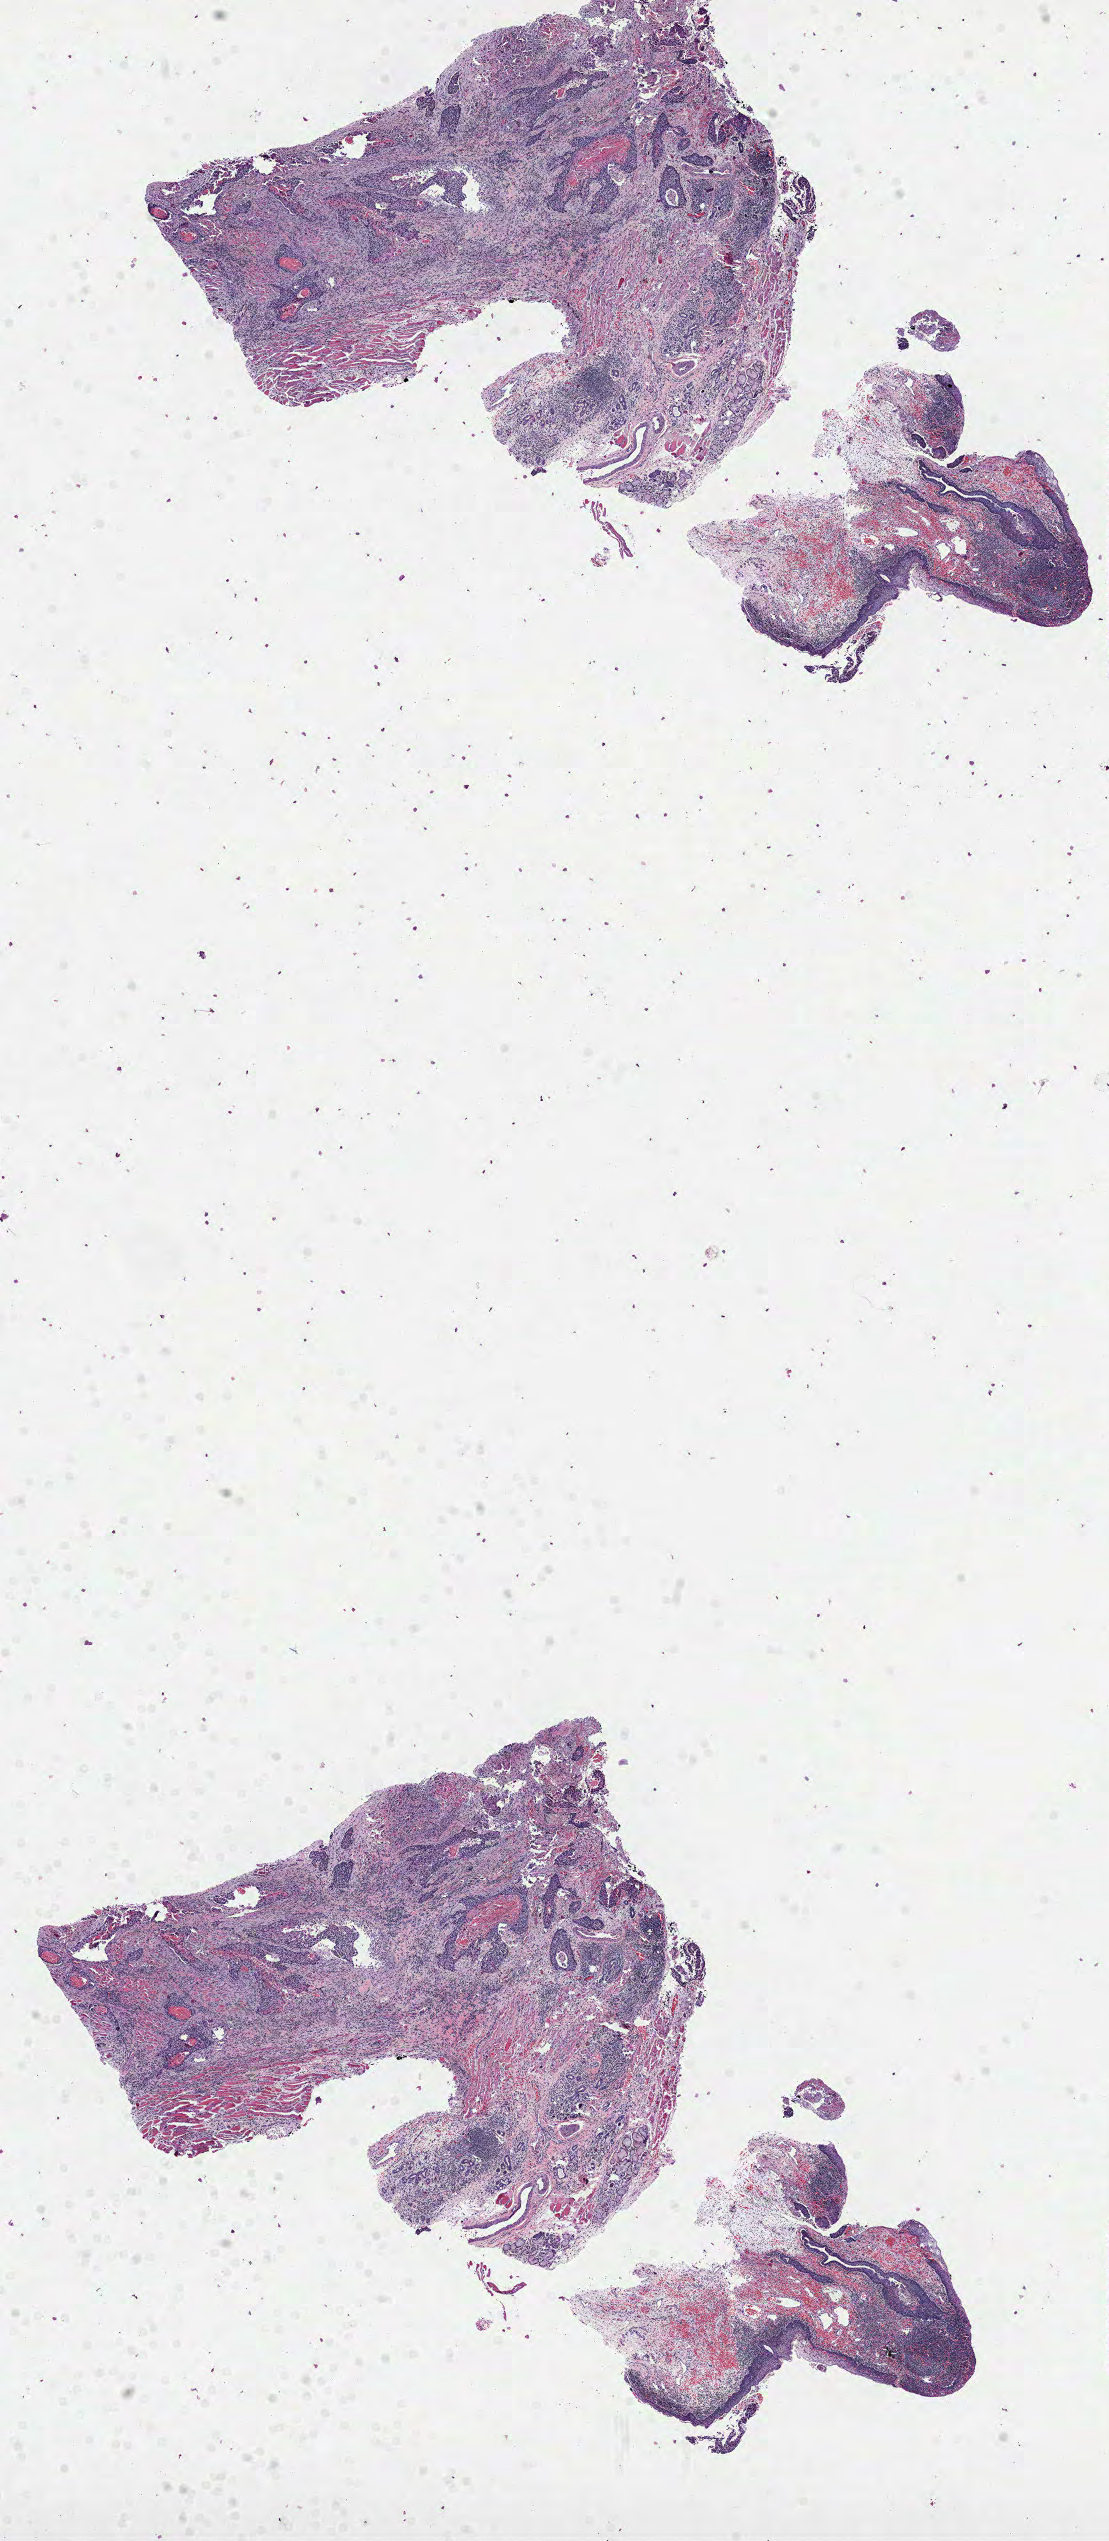
H&E-stained whole-slide image — a low-resolution overview of the entire scanned area, about 8.9 x 20.5 mm (slide scanned at 40x), formalin-fixed paraffin-embedded (FFPE) diagnostic section, sample: primary tumour, head and neck. Male, age 56 years at initial diagnosis. Histologic grade: G2 (moderately differentiated).
Histologic diagnosis: Squamous cell carcinoma, NOS (overlapping lesion of lip, oral cavity and pharynx). AJCC pathologic stage: IVA (7th edition). TNM: T3 N2b.